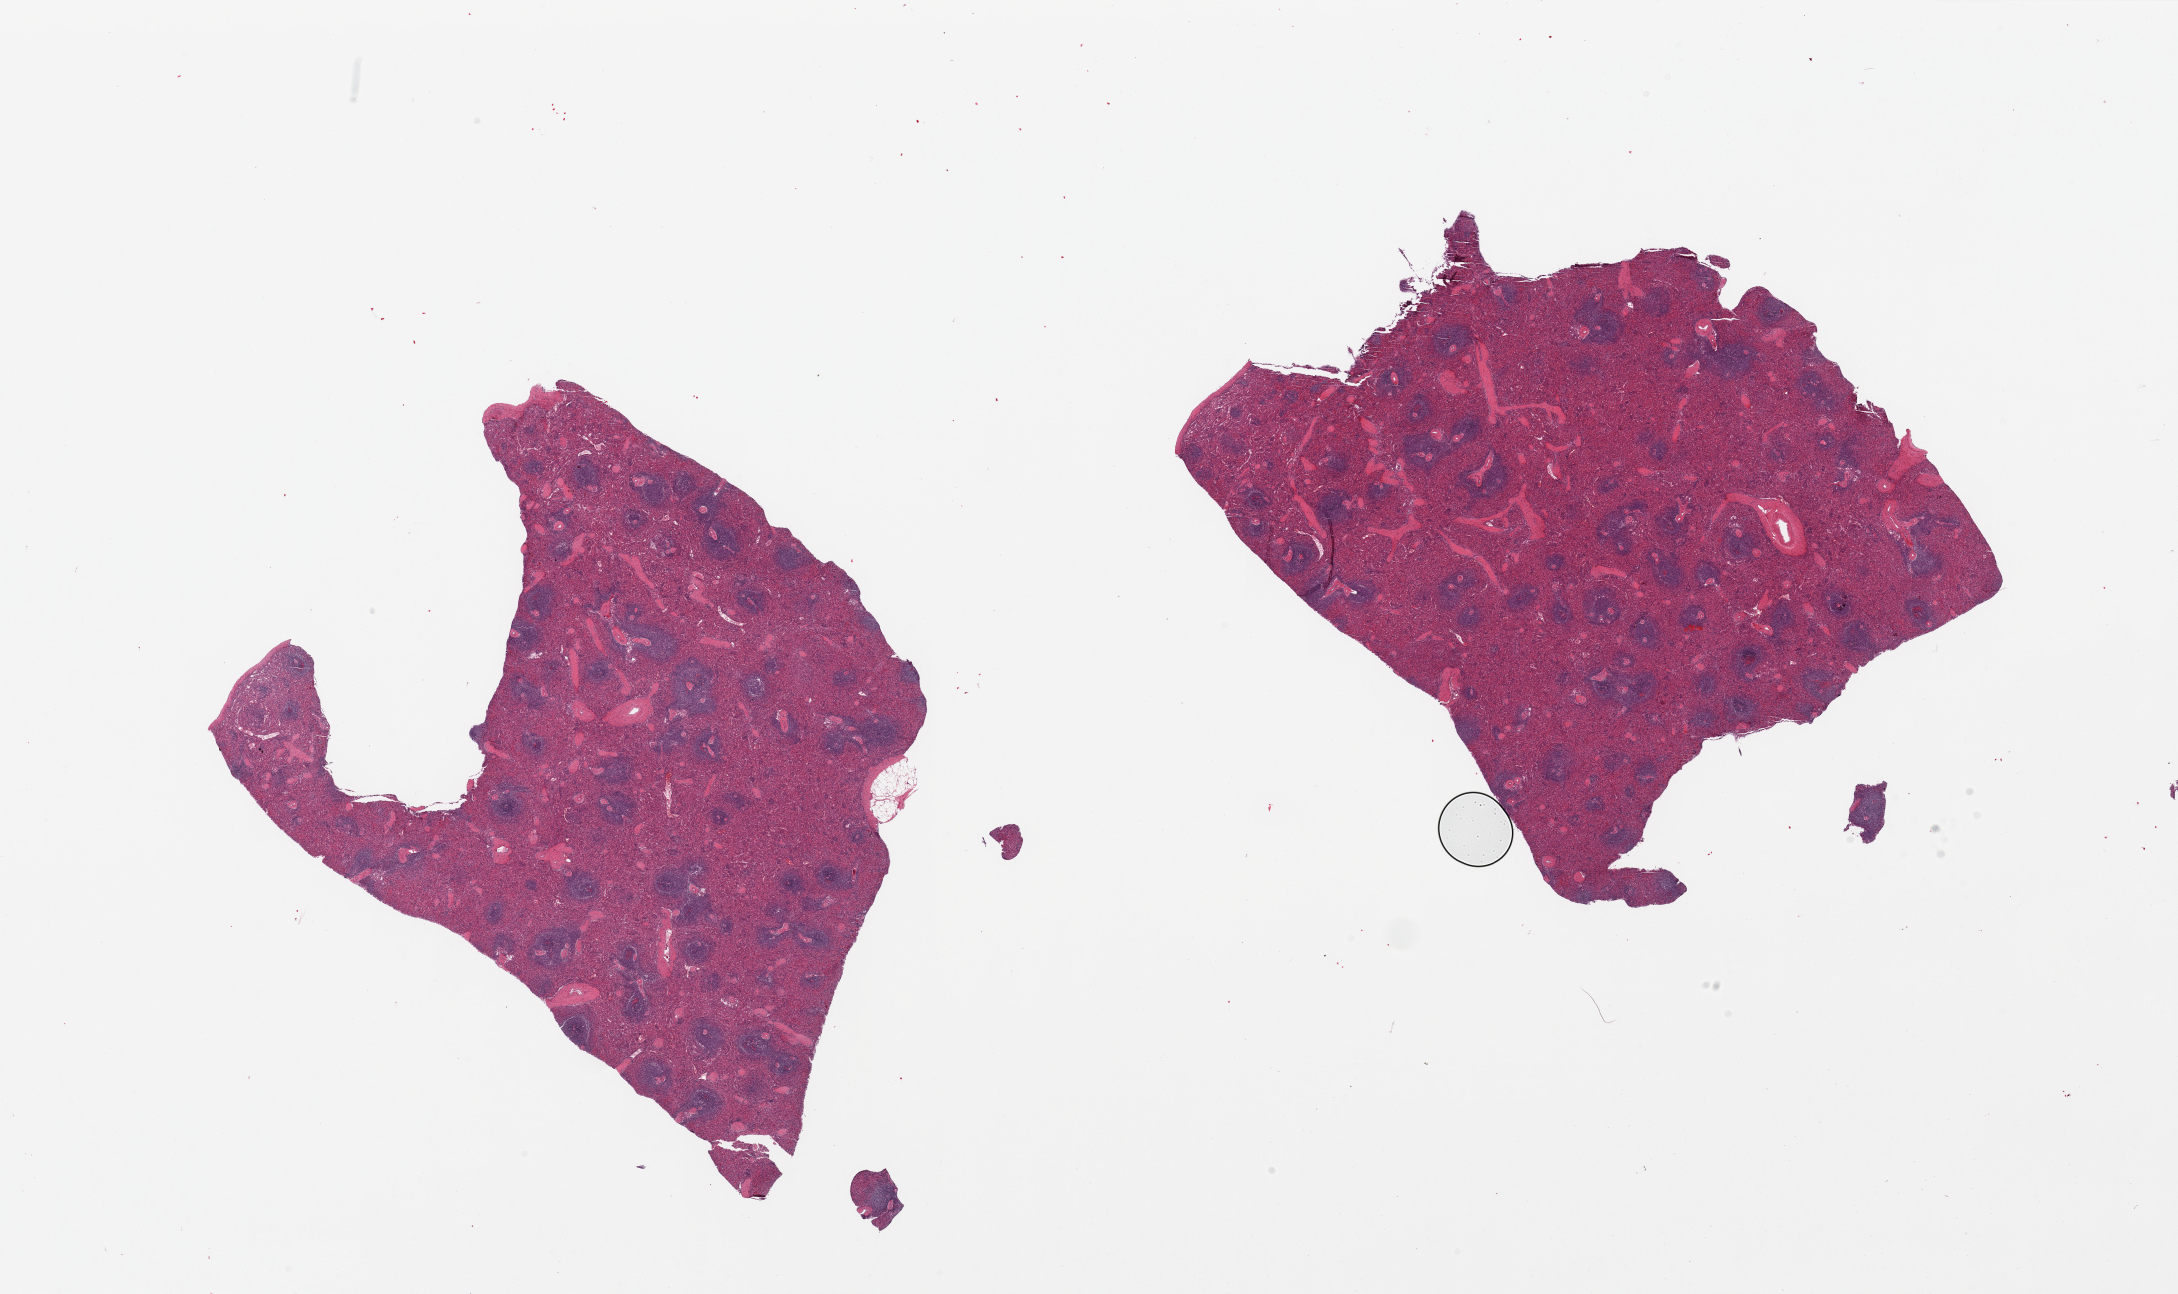
Digitized haematoxylin and eosin-stained section — shown as a low-resolution overview of the whole scanned area (about 34.5 x 20.5 mm, from a 20x scan), PAXgene-fixed, paraffin-embedded tissue, target tissue: spleen, tissue donor sample. Donor sex: female.
Review note (as recorded): 2 pieces, mild congestion.